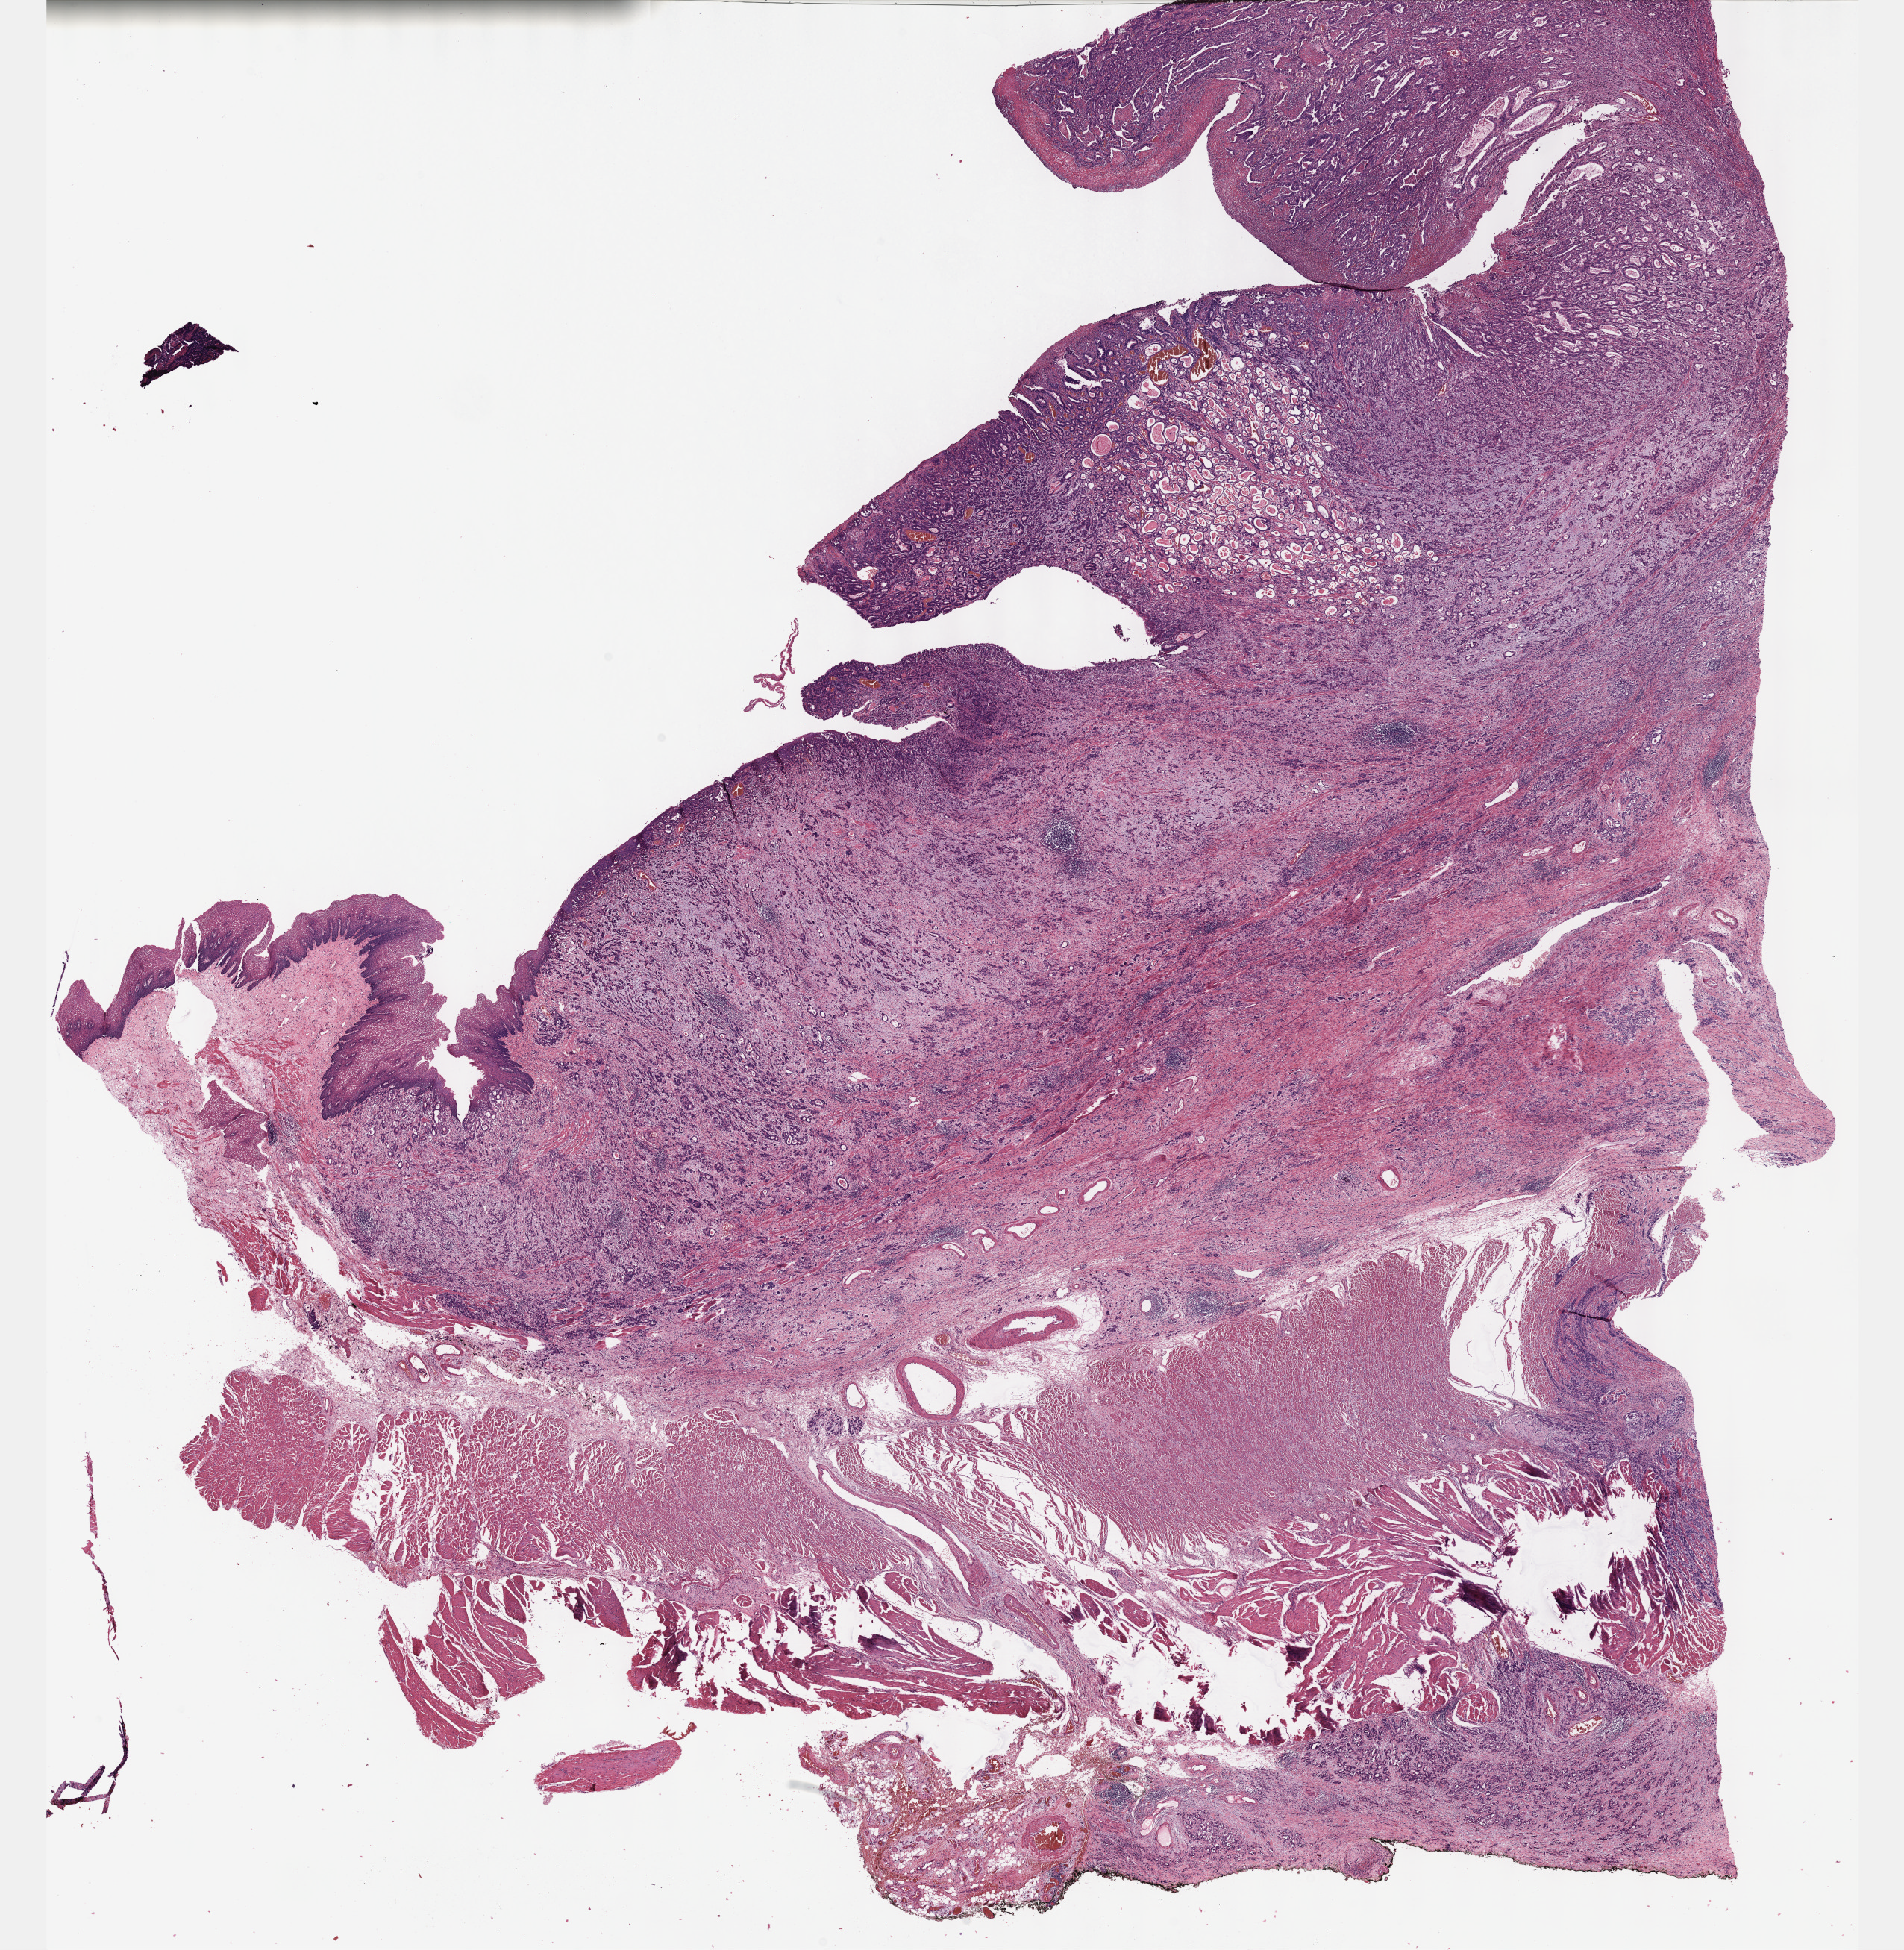
Digitized H&E tissue section (whole slide), whole scanned area (about 20.6 x 21.1 mm, from a 40x scan) shown as a low-resolution overview; FFPE section; primary tumour sample from the esophagus. Male patient; age at initial diagnosis 73 years. Histologic grade: G2 (moderately differentiated).
Lymph nodes positive (case pathology): 7 of 13 examined. AJCC pathologic stage: III (6th edition). Histologic diagnosis: Tubular adenocarcinoma (lower third of esophagus).